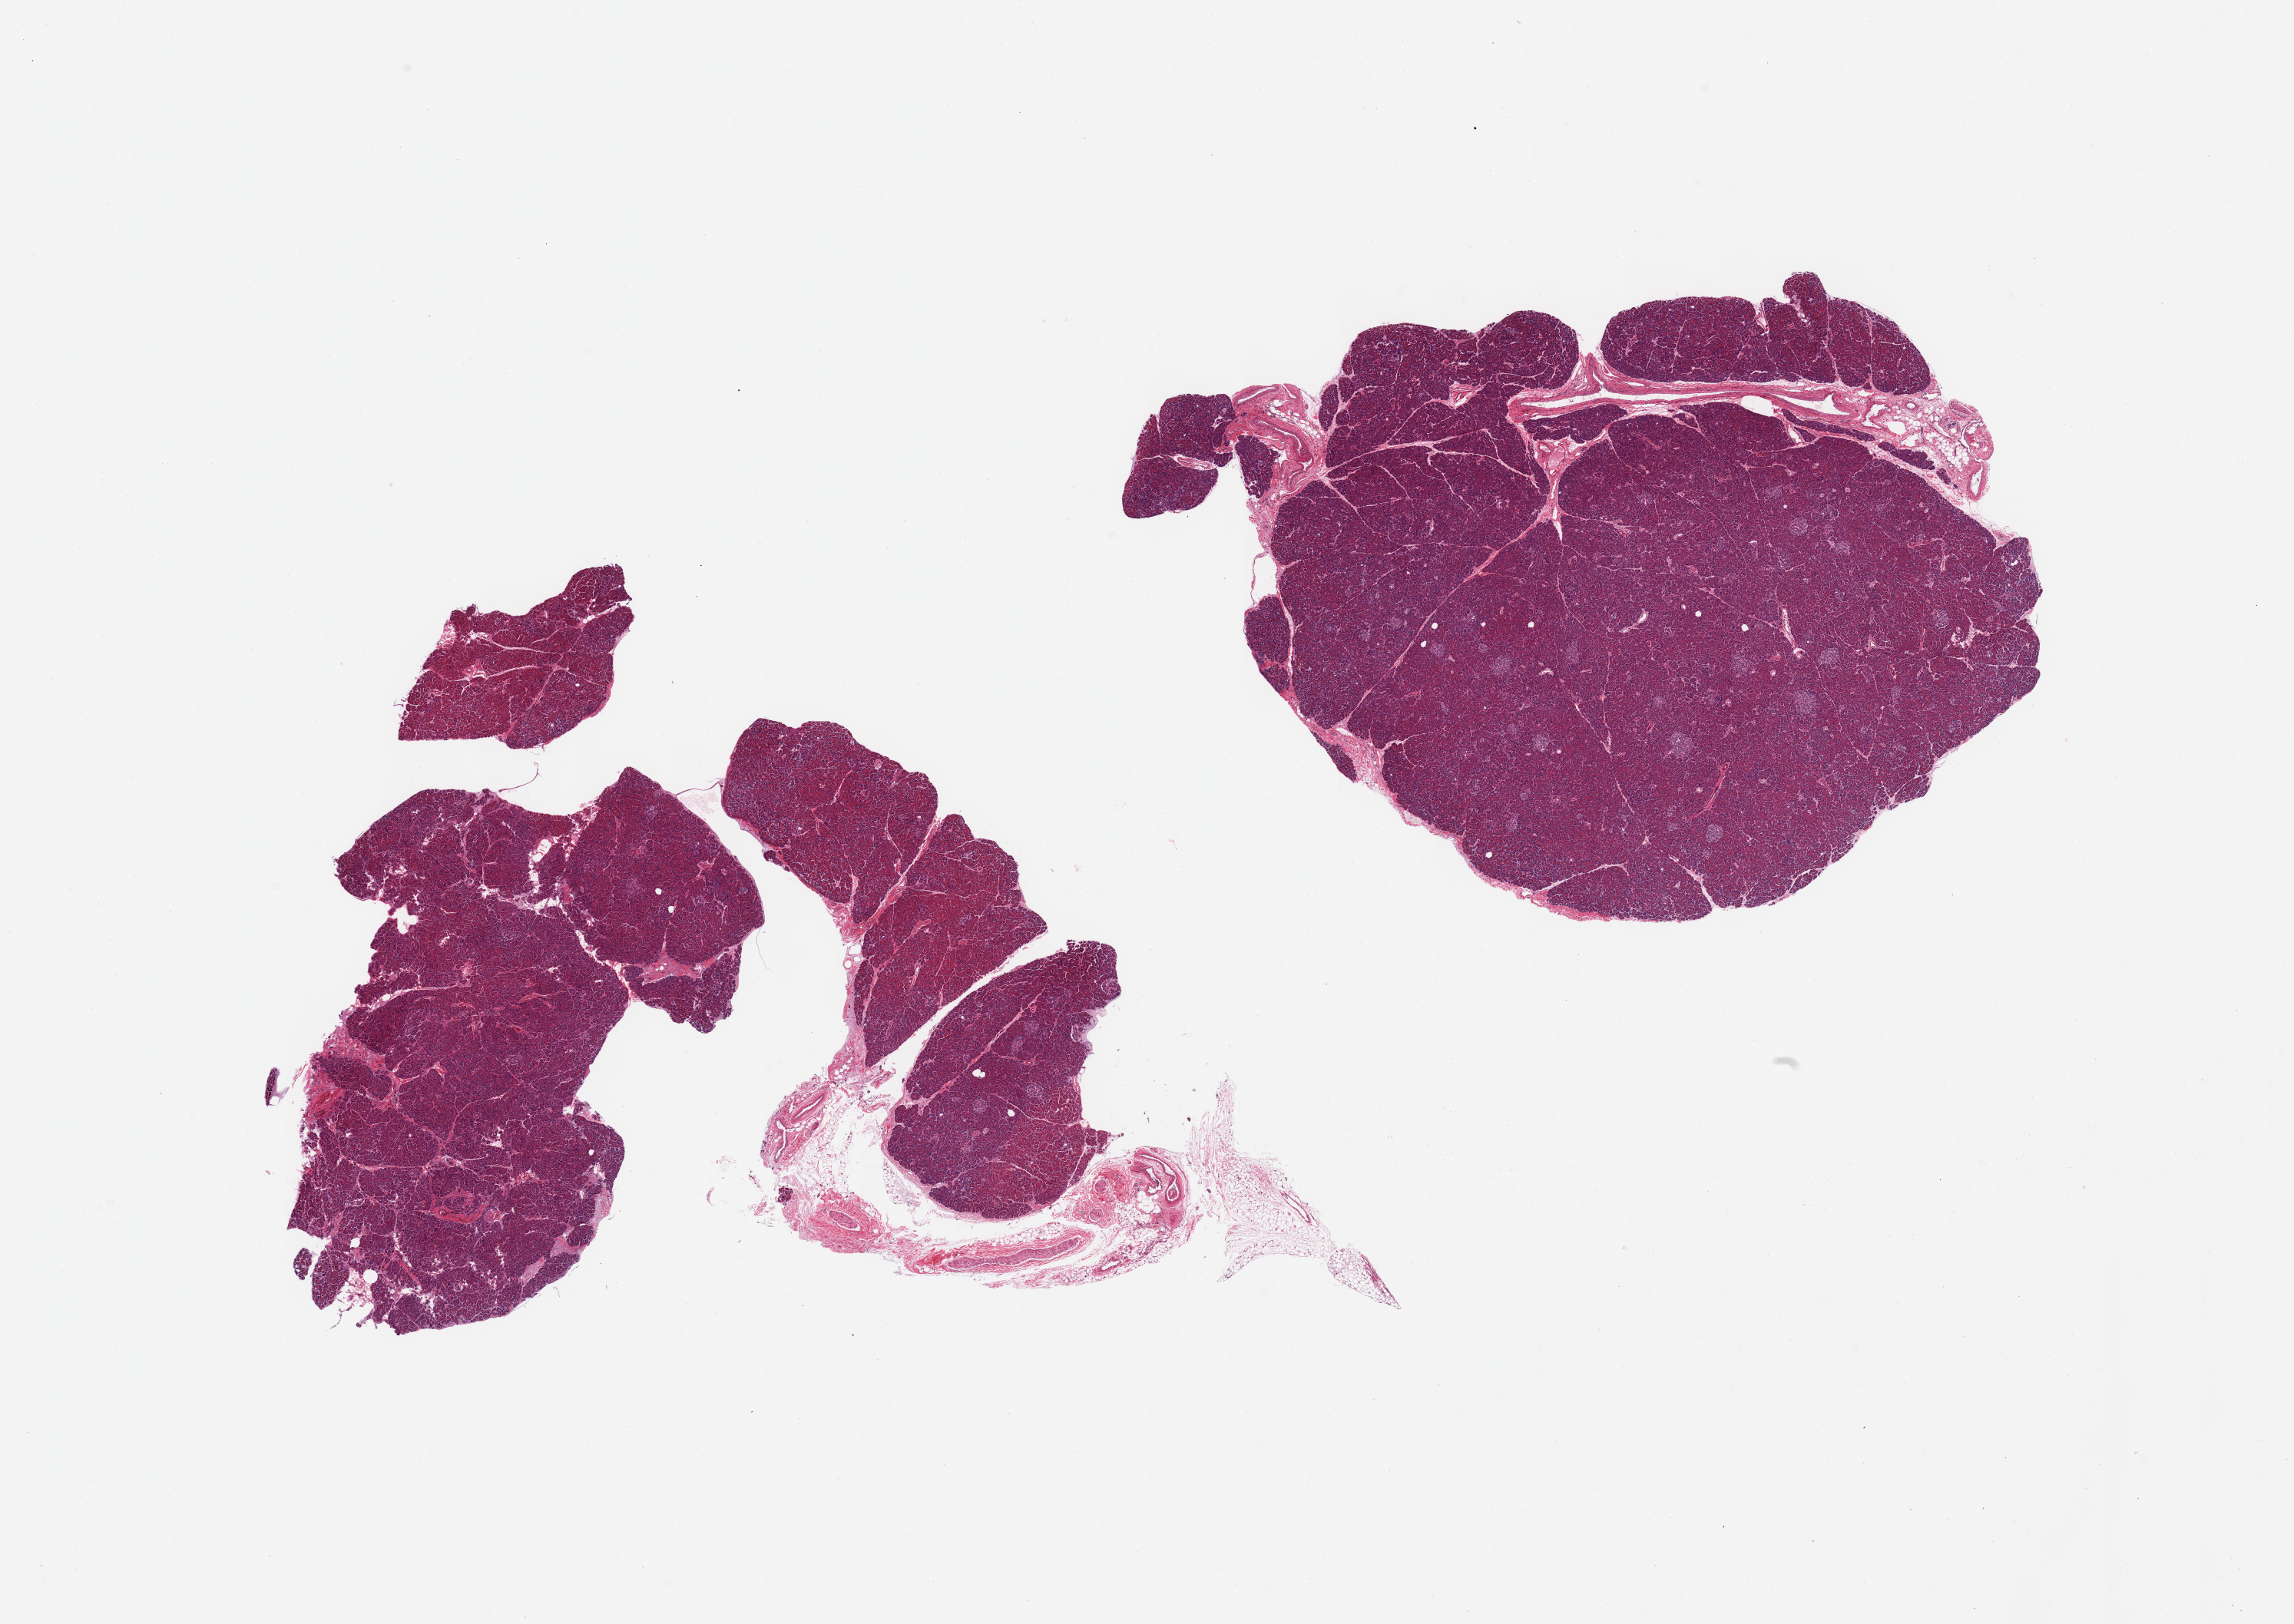
Whole-slide image, hematoxylin and eosin (H&E) stain — whole scanned area (about 23.6 x 16.7 mm, acquisition: 20x scan) shown as a low-resolution overview; PAXgene-fixed paraffin-embedded (PFPE) section; sampled site (target tissue): pancreas; tissue donor sample.
Reviewer comment on this tissue sample: 2 pieces; well preserved parenchyma; Langerhans islets present.